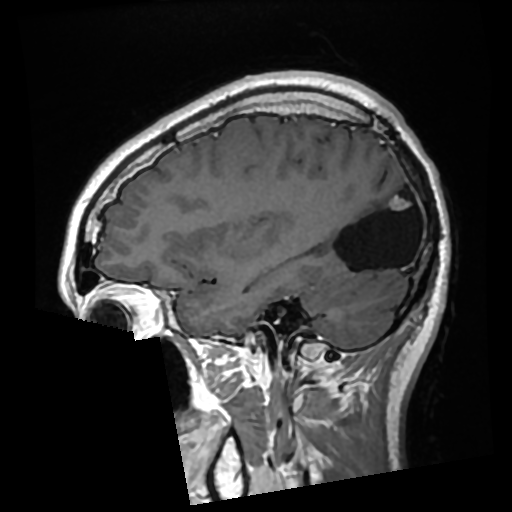
Brain MRI from a brain-tumour surgery series, one sagittal slice. Slice 92 of 276 in the series (ordered by position). T1-weighted post-contrast. 0.7 mm slice thickness. 512 × 512 image matrix, field of view 250 × 250 mm. From the clinical record (not read from this slice): histopathology: Glioma with ependymal features; WHO grade: 2.
Annotated regions visible in this slice (outlined manually by an expert reader):
- previous resection cavity: bounding box (x1, y1, x2, y2) in pixels: (326, 182, 413, 270)
- tumour: (390, 197, 410, 211)